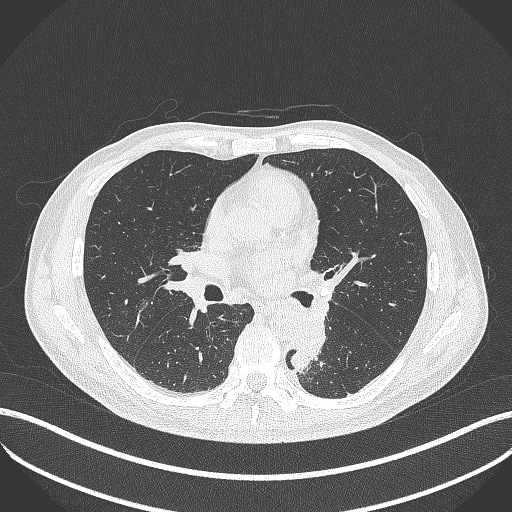
Chest CT, one axial slice; slice 219 of 451 in the series (ordered by position); reconstruction kernel B70f; lung window (W 1500 / L -600 HU); 1 mm slice thickness; 512 × 512 image matrix. Male patient, age 72 years. Case-level facts recorded for this patient, not image findings: clinical TNM (as recorded): T2b N0 M1.
Outlined on this slice (rectangle marked by the reading radiologist):
- lung tumour (recorded histology: adenocarcinoma): box from (x=290, y=319) to (x=329, y=372) px